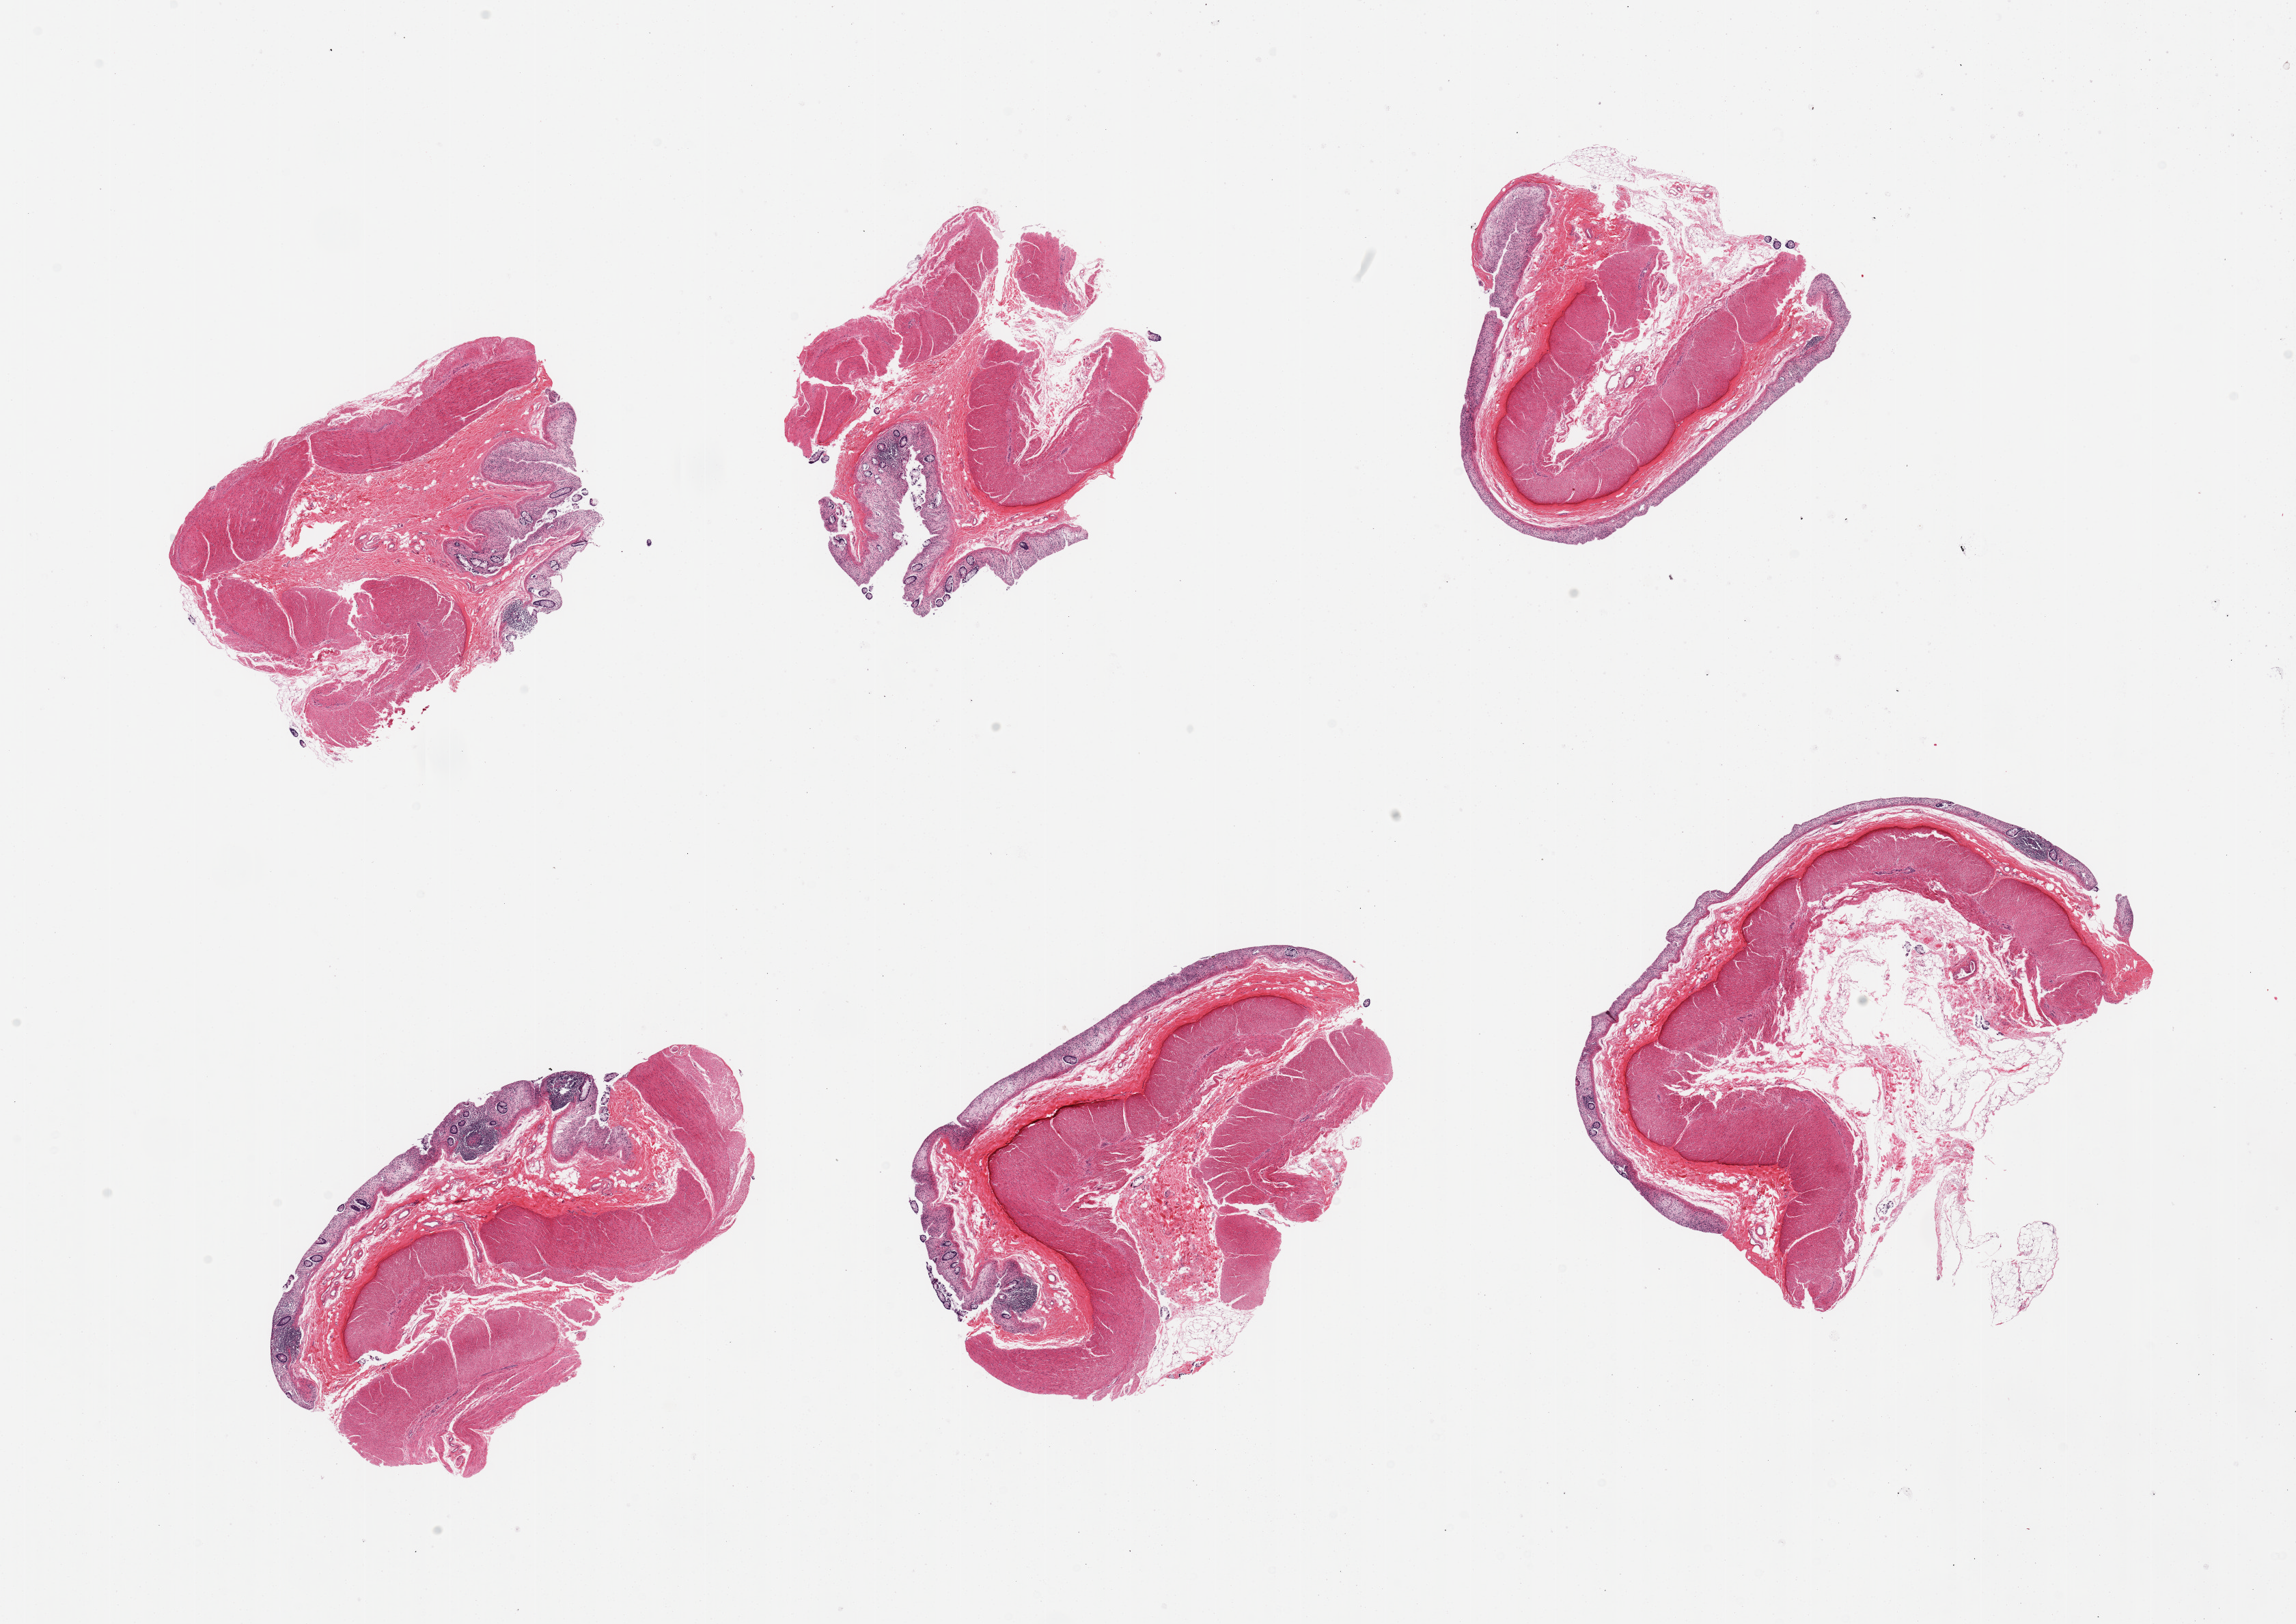
Digitized haematoxylin and eosin-stained section, low-resolution overview of the scanned area, about 26.6 x 18.8 mm (from a 20x scan); PAXgene-fixed, paraffin-embedded tissue; target tissue: transverse colon; tissue donor sample.
- reviewer comment on this tissue sample: 6 pieces; autolyzed mucosa, preserved muscle & submucosa